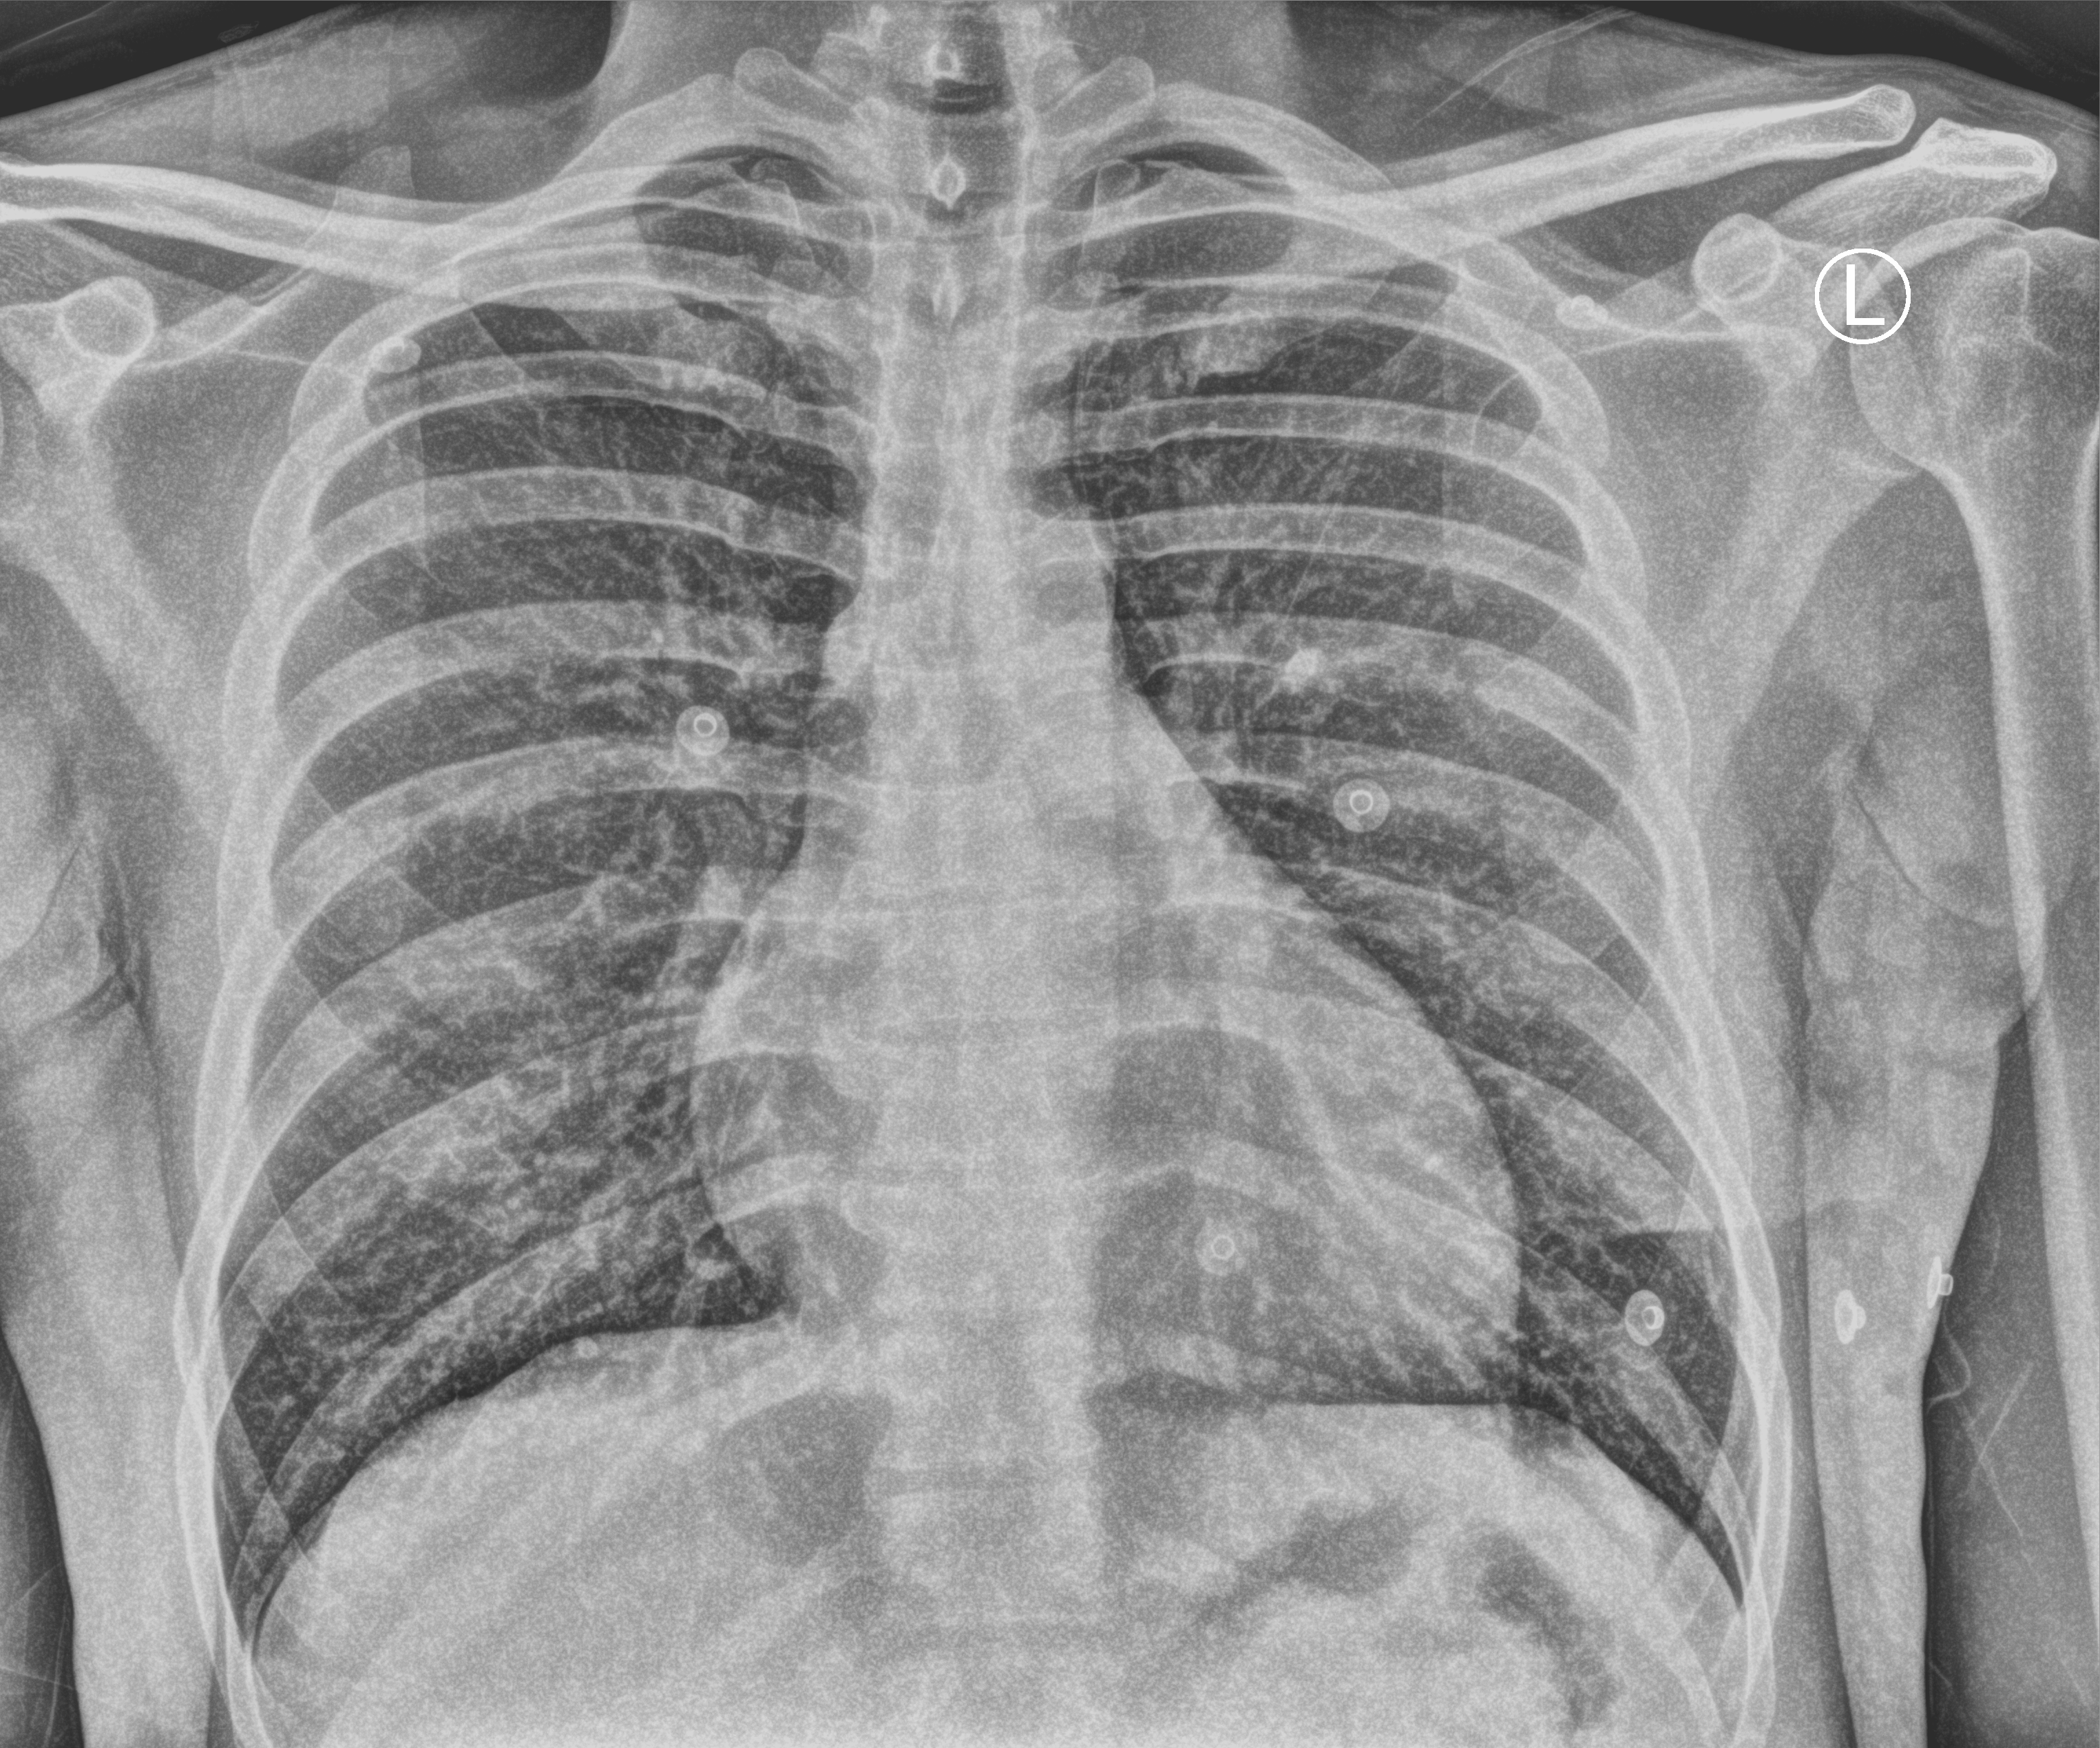
Bedside chest radiograph (computed radiography). Male patient hospitalised with COVID-19, age 18–59 years.
Hospital-stay facts (about this admission, not read from this image; timing relative to this image not recorded): mechanically ventilated during this hospital stay: no.